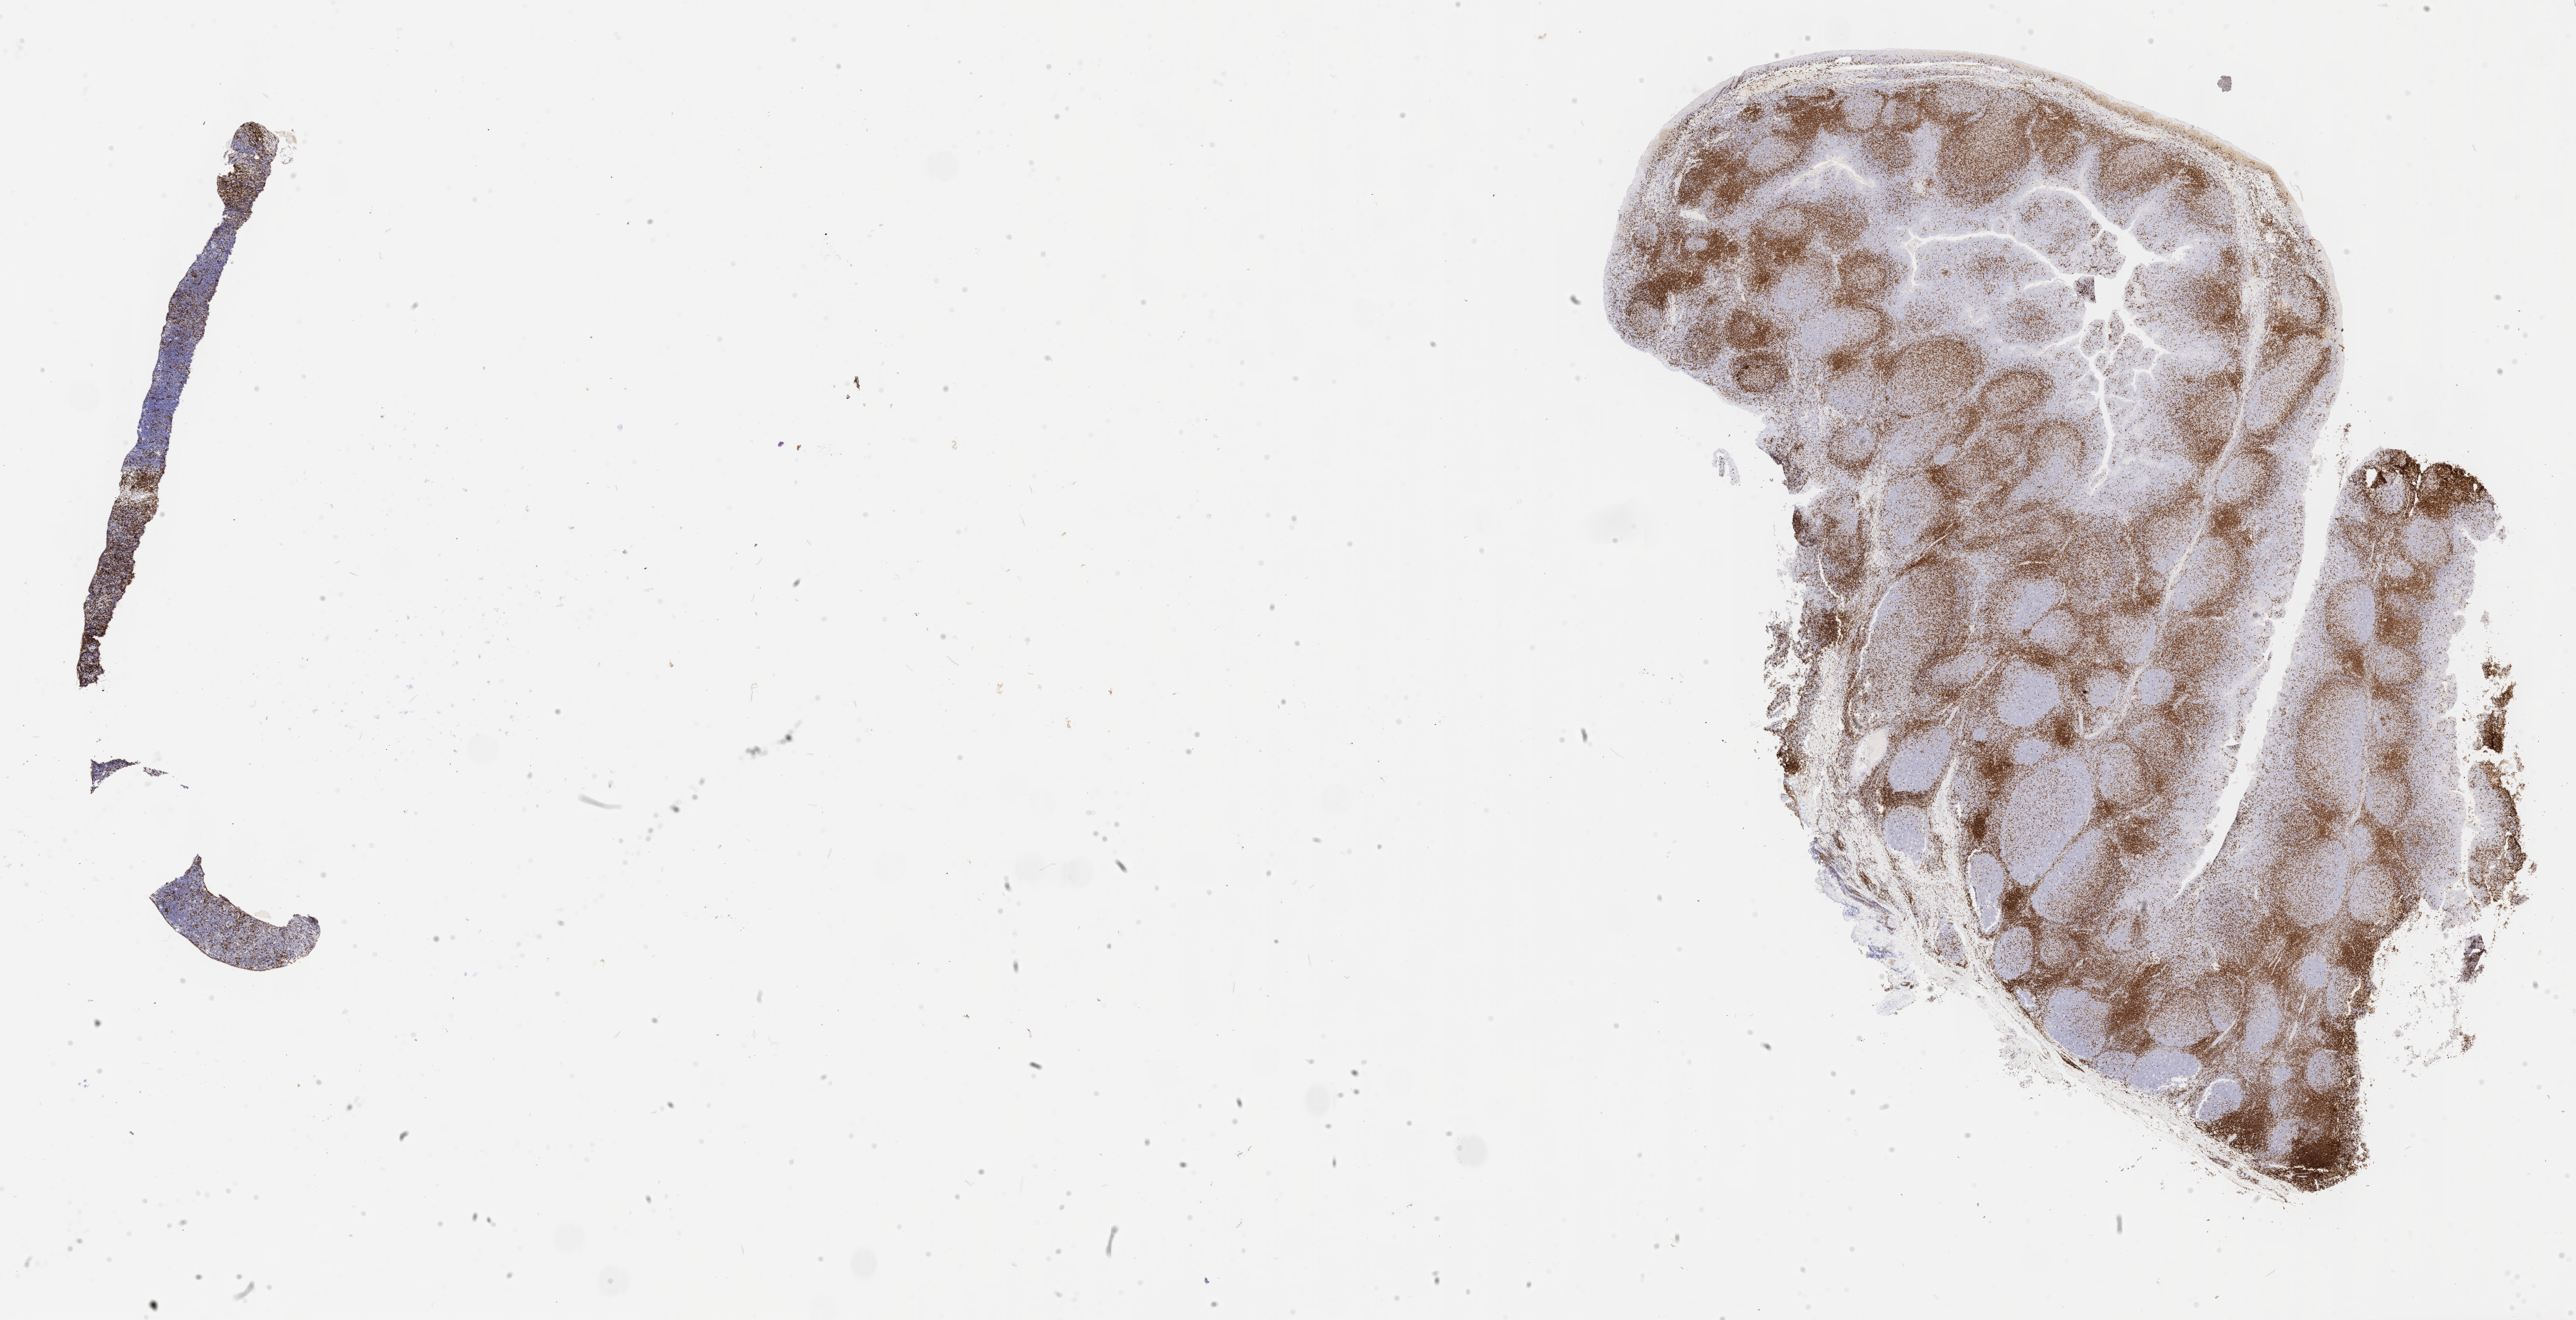
Immunohistochemistry (IHC) whole-slide image stained for CD3, low-resolution overview of the scanned area, about 29.2 x 15.0 mm. Specimen: tumor tissue. Site: ovary. Patient: female, age at initial diagnosis 9 years.
• histologic diagnosis: Burkitt lymphoma, NOS